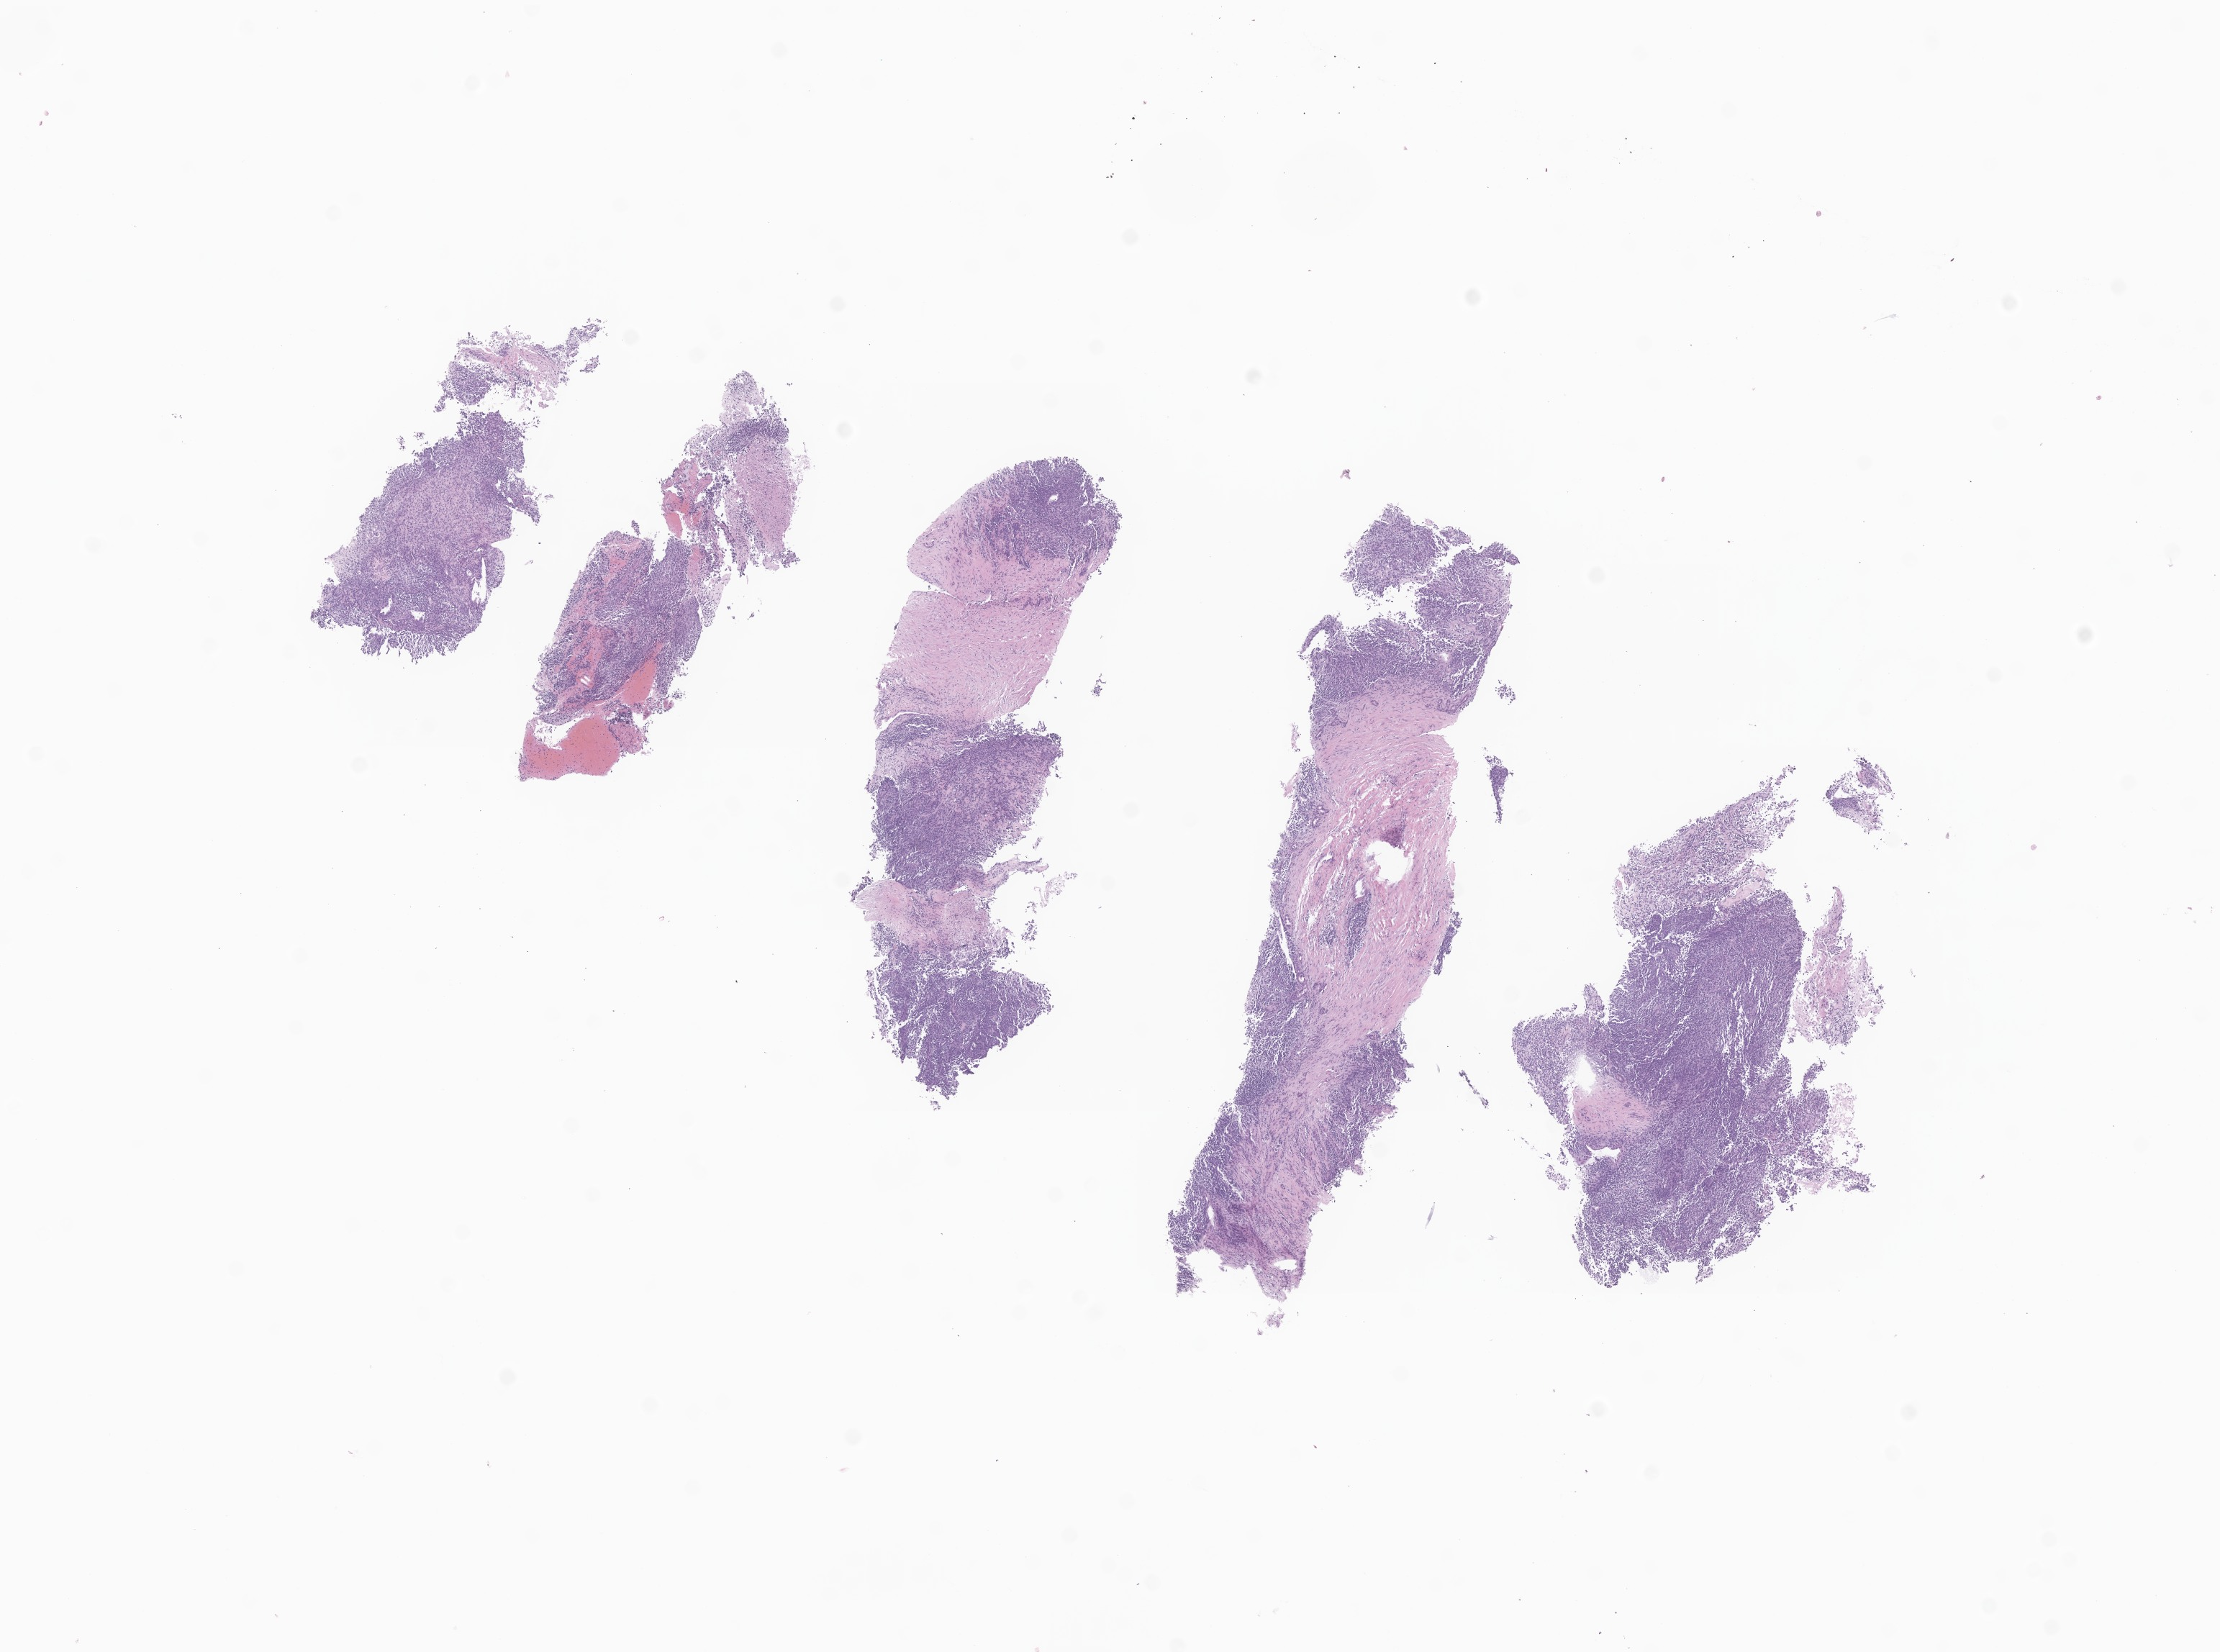
Digitized H&E-stained section of tumor tissue from the liver — a low-resolution overview of the entire scanned area, about 13.0 x 9.7 mm, formalin-fixed, paraffin-embedded (FFPE) tissue. Male patient, age 199 days.
Diagnosis (ICD-O-3 morphology term): Rhabdoid tumor, NOS.